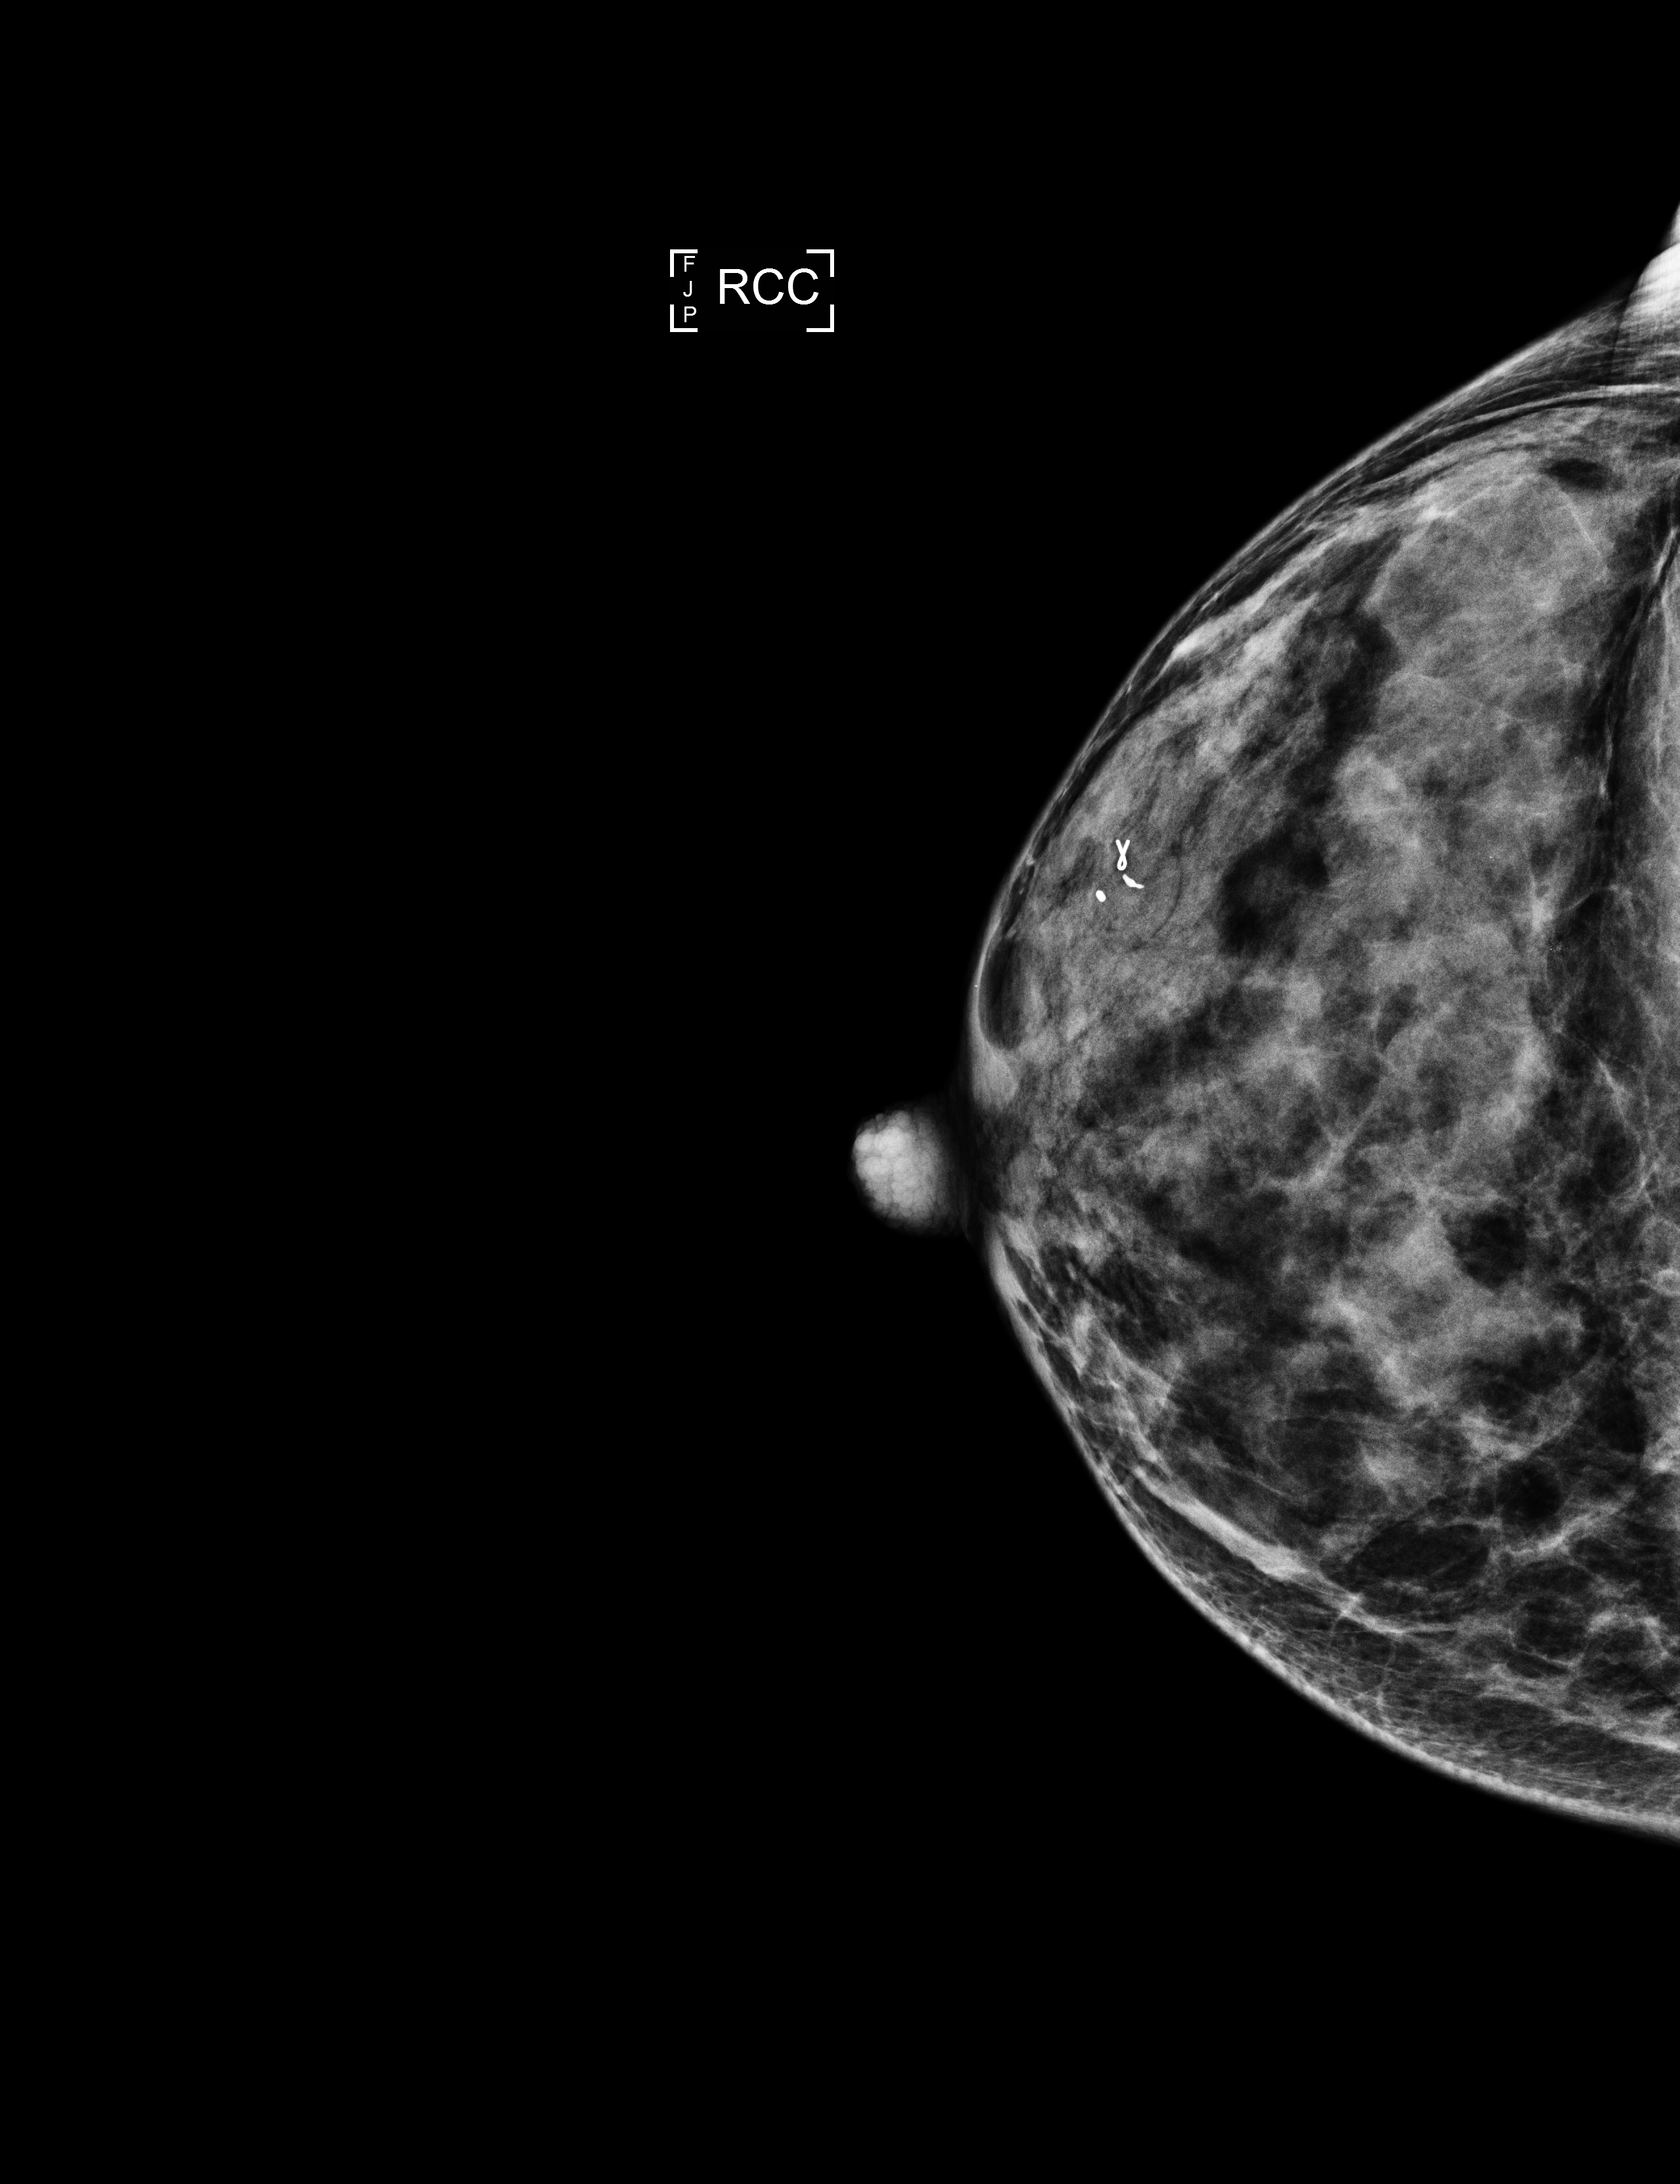
Full-field digital mammogram (FFDM); right breast; cranio-caudal projection; screening examination; compressed breast thickness 35 mm; system: Selenia Dimensions. Patient aged 53 years (female).
Breast density at the screening exam (both breasts): extremely dense (BI-RADS density category d). Final BI-RADS assessment for this screening round (tomosynthesis exam, both breasts): category 2. Recall: no recall after this screen.